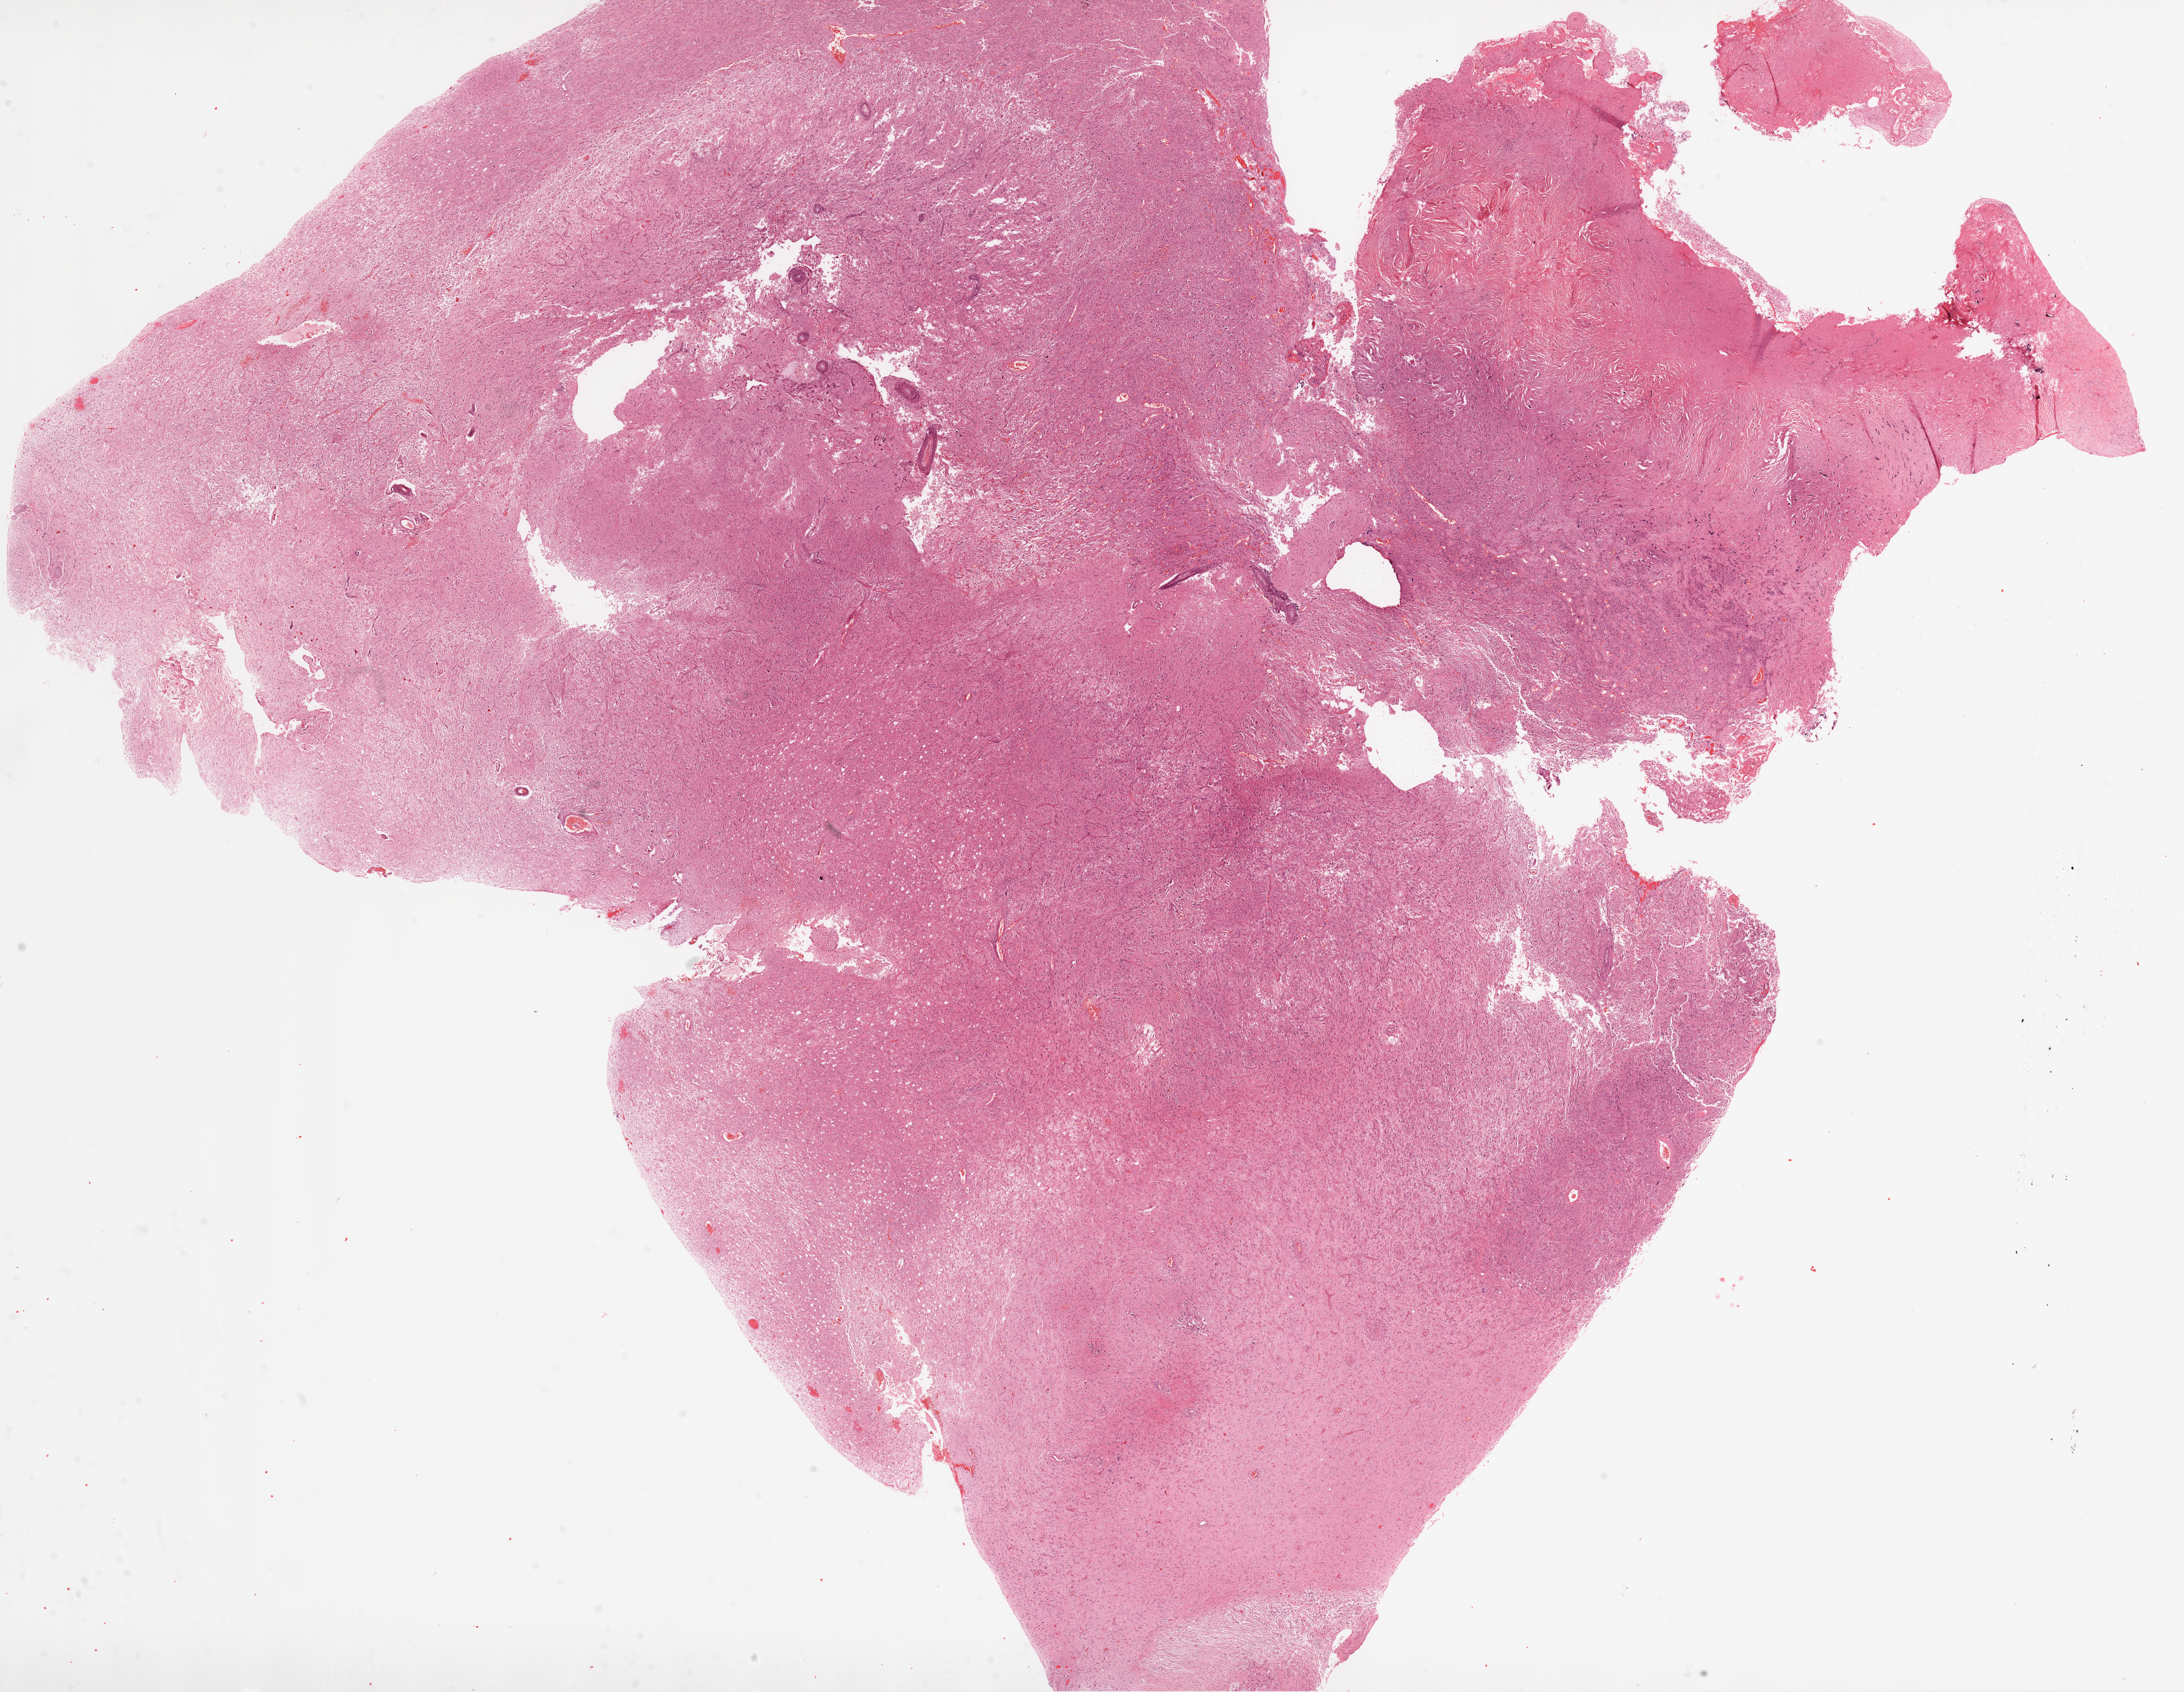
H&E-stained whole-slide image, whole scanned area (about 27.1 x 21.0 mm) shown as a low-resolution overview. Formalin-fixed paraffin-embedded (FFPE) diagnostic section. Primary tumour sample from the brain. Female, age 44 years at initial diagnosis.
Diagnosis: Glioblastoma.